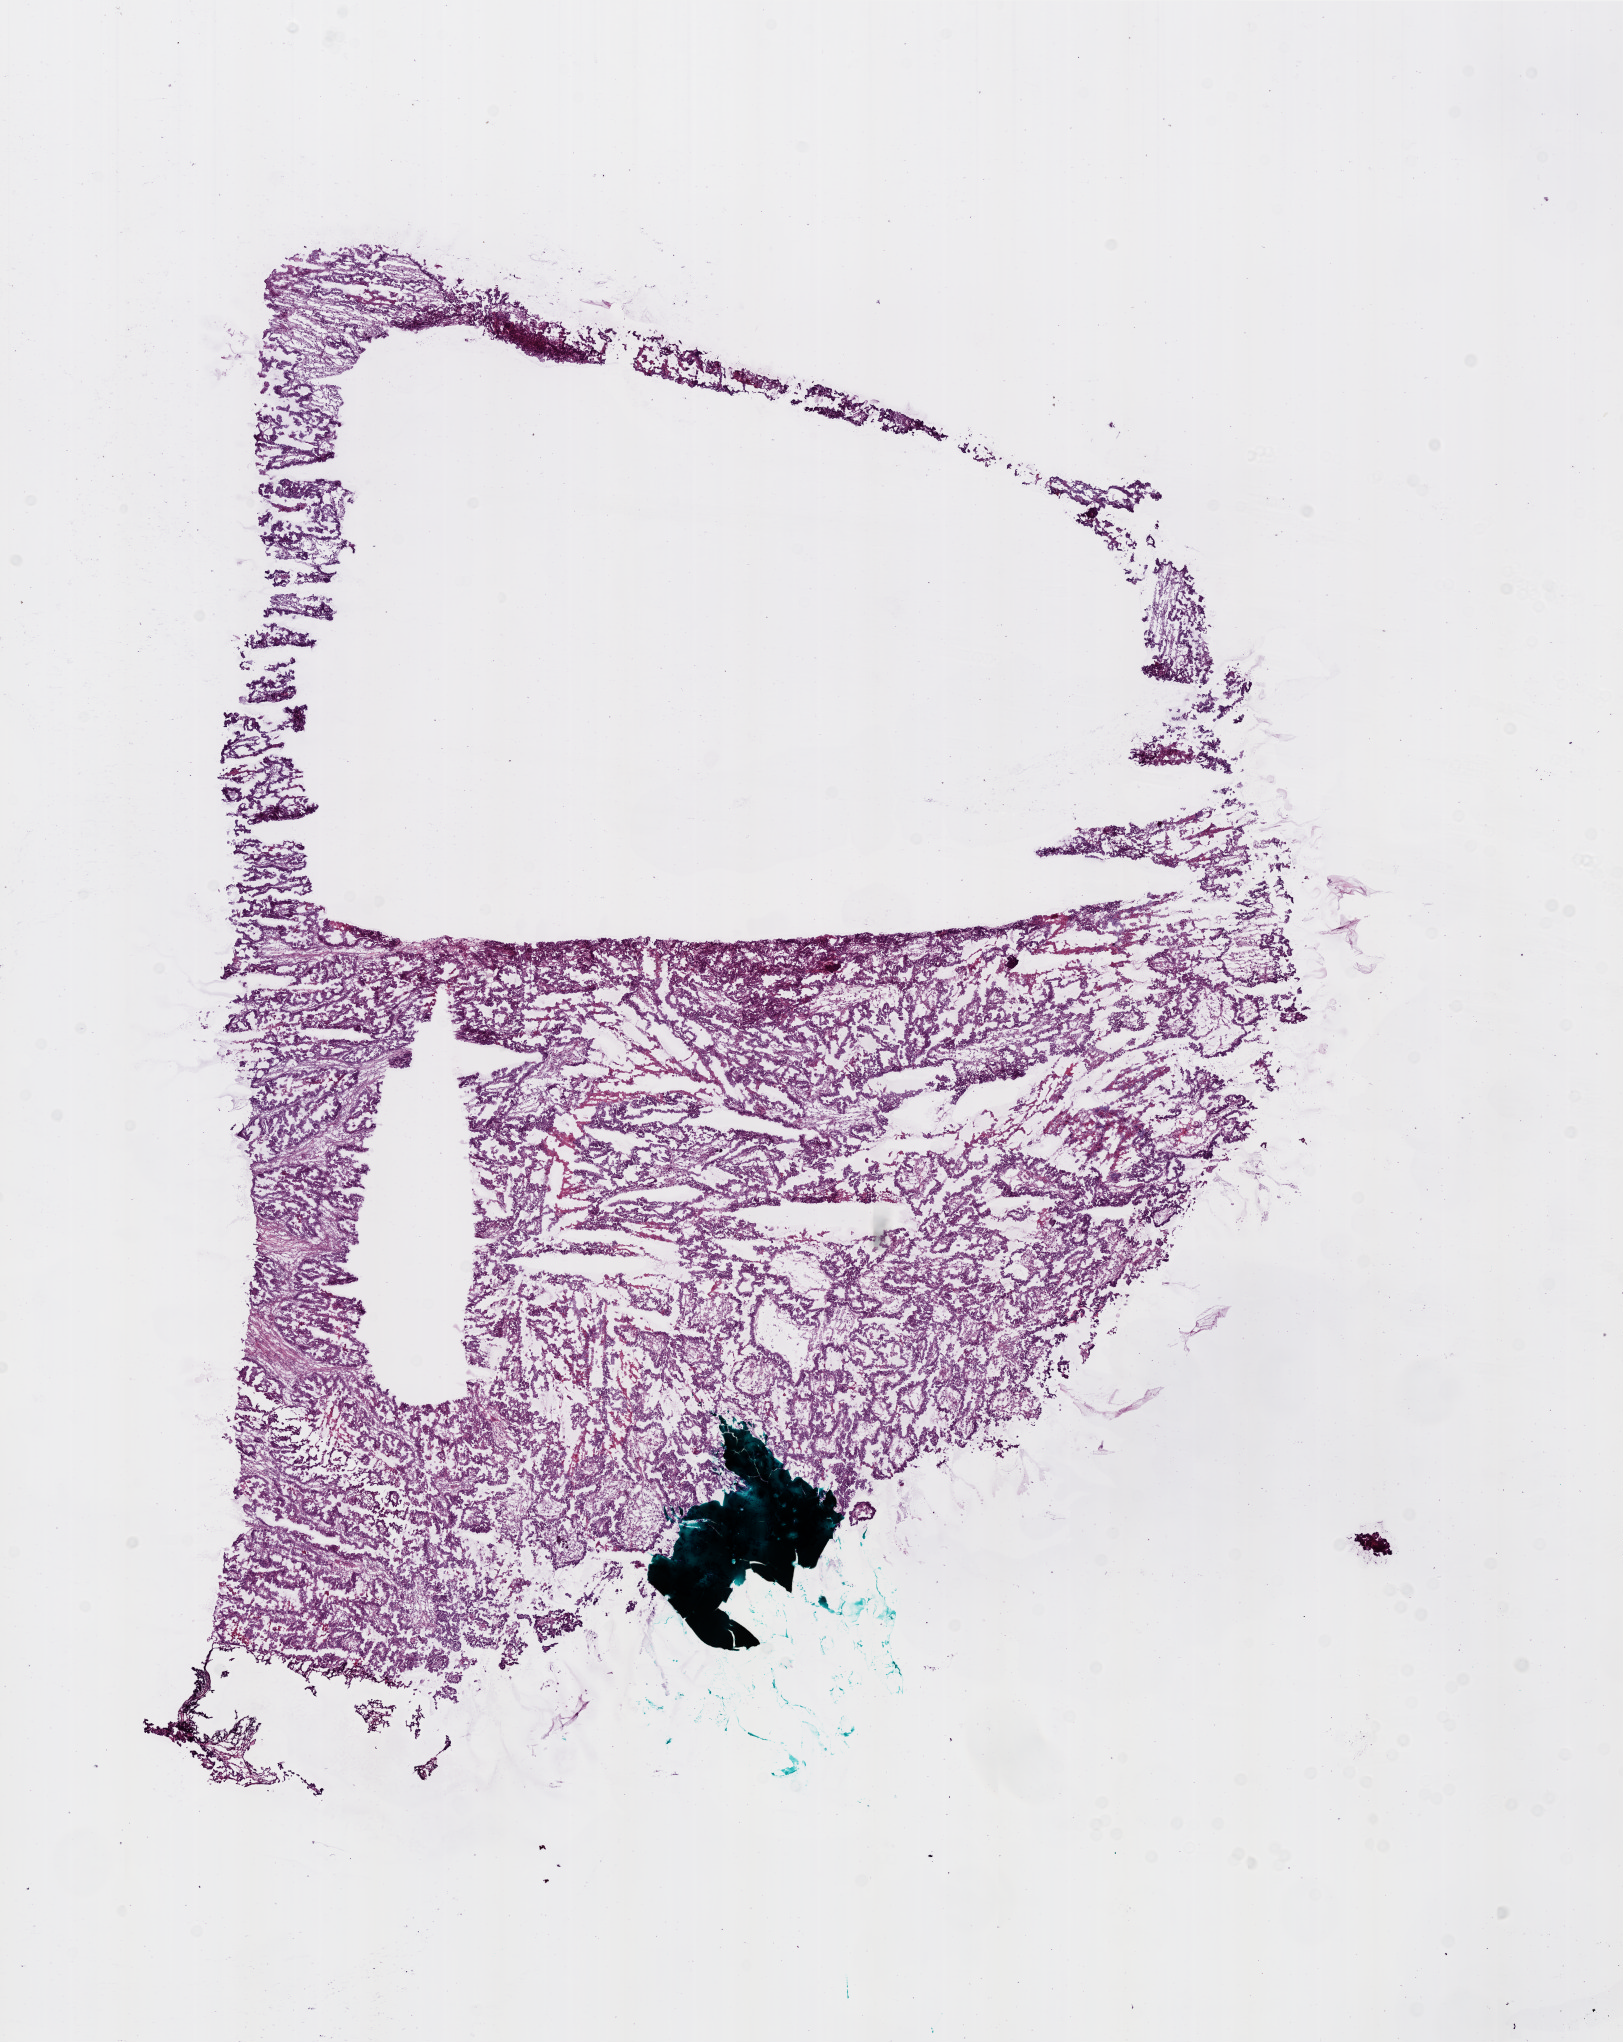
H&E whole-slide image, a low-resolution overview of the entire scanned area, about 13.0 x 16.3 mm (from a 20x scan); frozen section from the bottom of the tissue portion; primary tumour sample from the ovary. Female patient; age at initial diagnosis 42 years. Histologic grade: G3 (poorly differentiated). Composition of this section per pathologist review: tumour cells 85%, tumour nuclei 95%, normal cells 5%, stromal cells 0%, necrosis 10%.
Pathologic diagnosis: Serous cystadenocarcinoma, NOS. FIGO stage: IIIC.